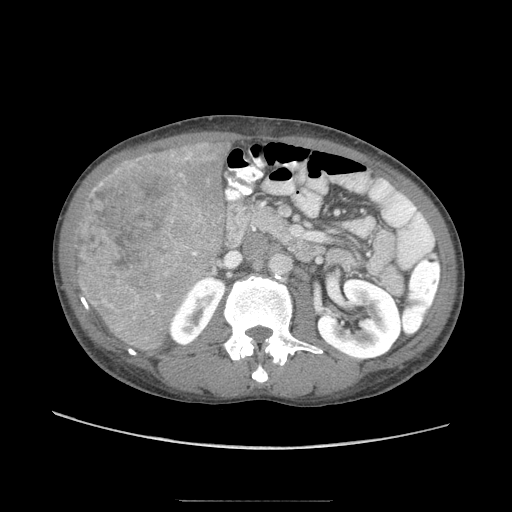
Contrast-enhanced abdominal CT (liver protocol), one axial slice. Slice 25 of 103 in the series (ordered by position). 120 kVp. Soft-tissue window (W 400 / L 40 HU). 512 × 512 image matrix, field of view 380 × 380 mm. From the clinical record (not read from this slice): diagnosis: hepatocellular carcinoma (patient treated with transarterial chemoembolisation; whether this scan precedes or follows treatment is not stated here); TNM stage (as recorded): Stage-IIIA; Child-Pugh class: A; tumour differentiation: moderately differentiated; tumour nodularity: multinodular.
Annotated regions visible in this slice (semi-automatic segmentation, software-assisted and operator-edited):
- liver parenchyma outside the tumour (the mass and vessels are separate outlines, so this box may not span the whole liver): bounding box <90,140,232,352> (left, top, right, bottom; pixels)
- mass: <72,152,207,323>
- liver vessels: <148,153,152,157>